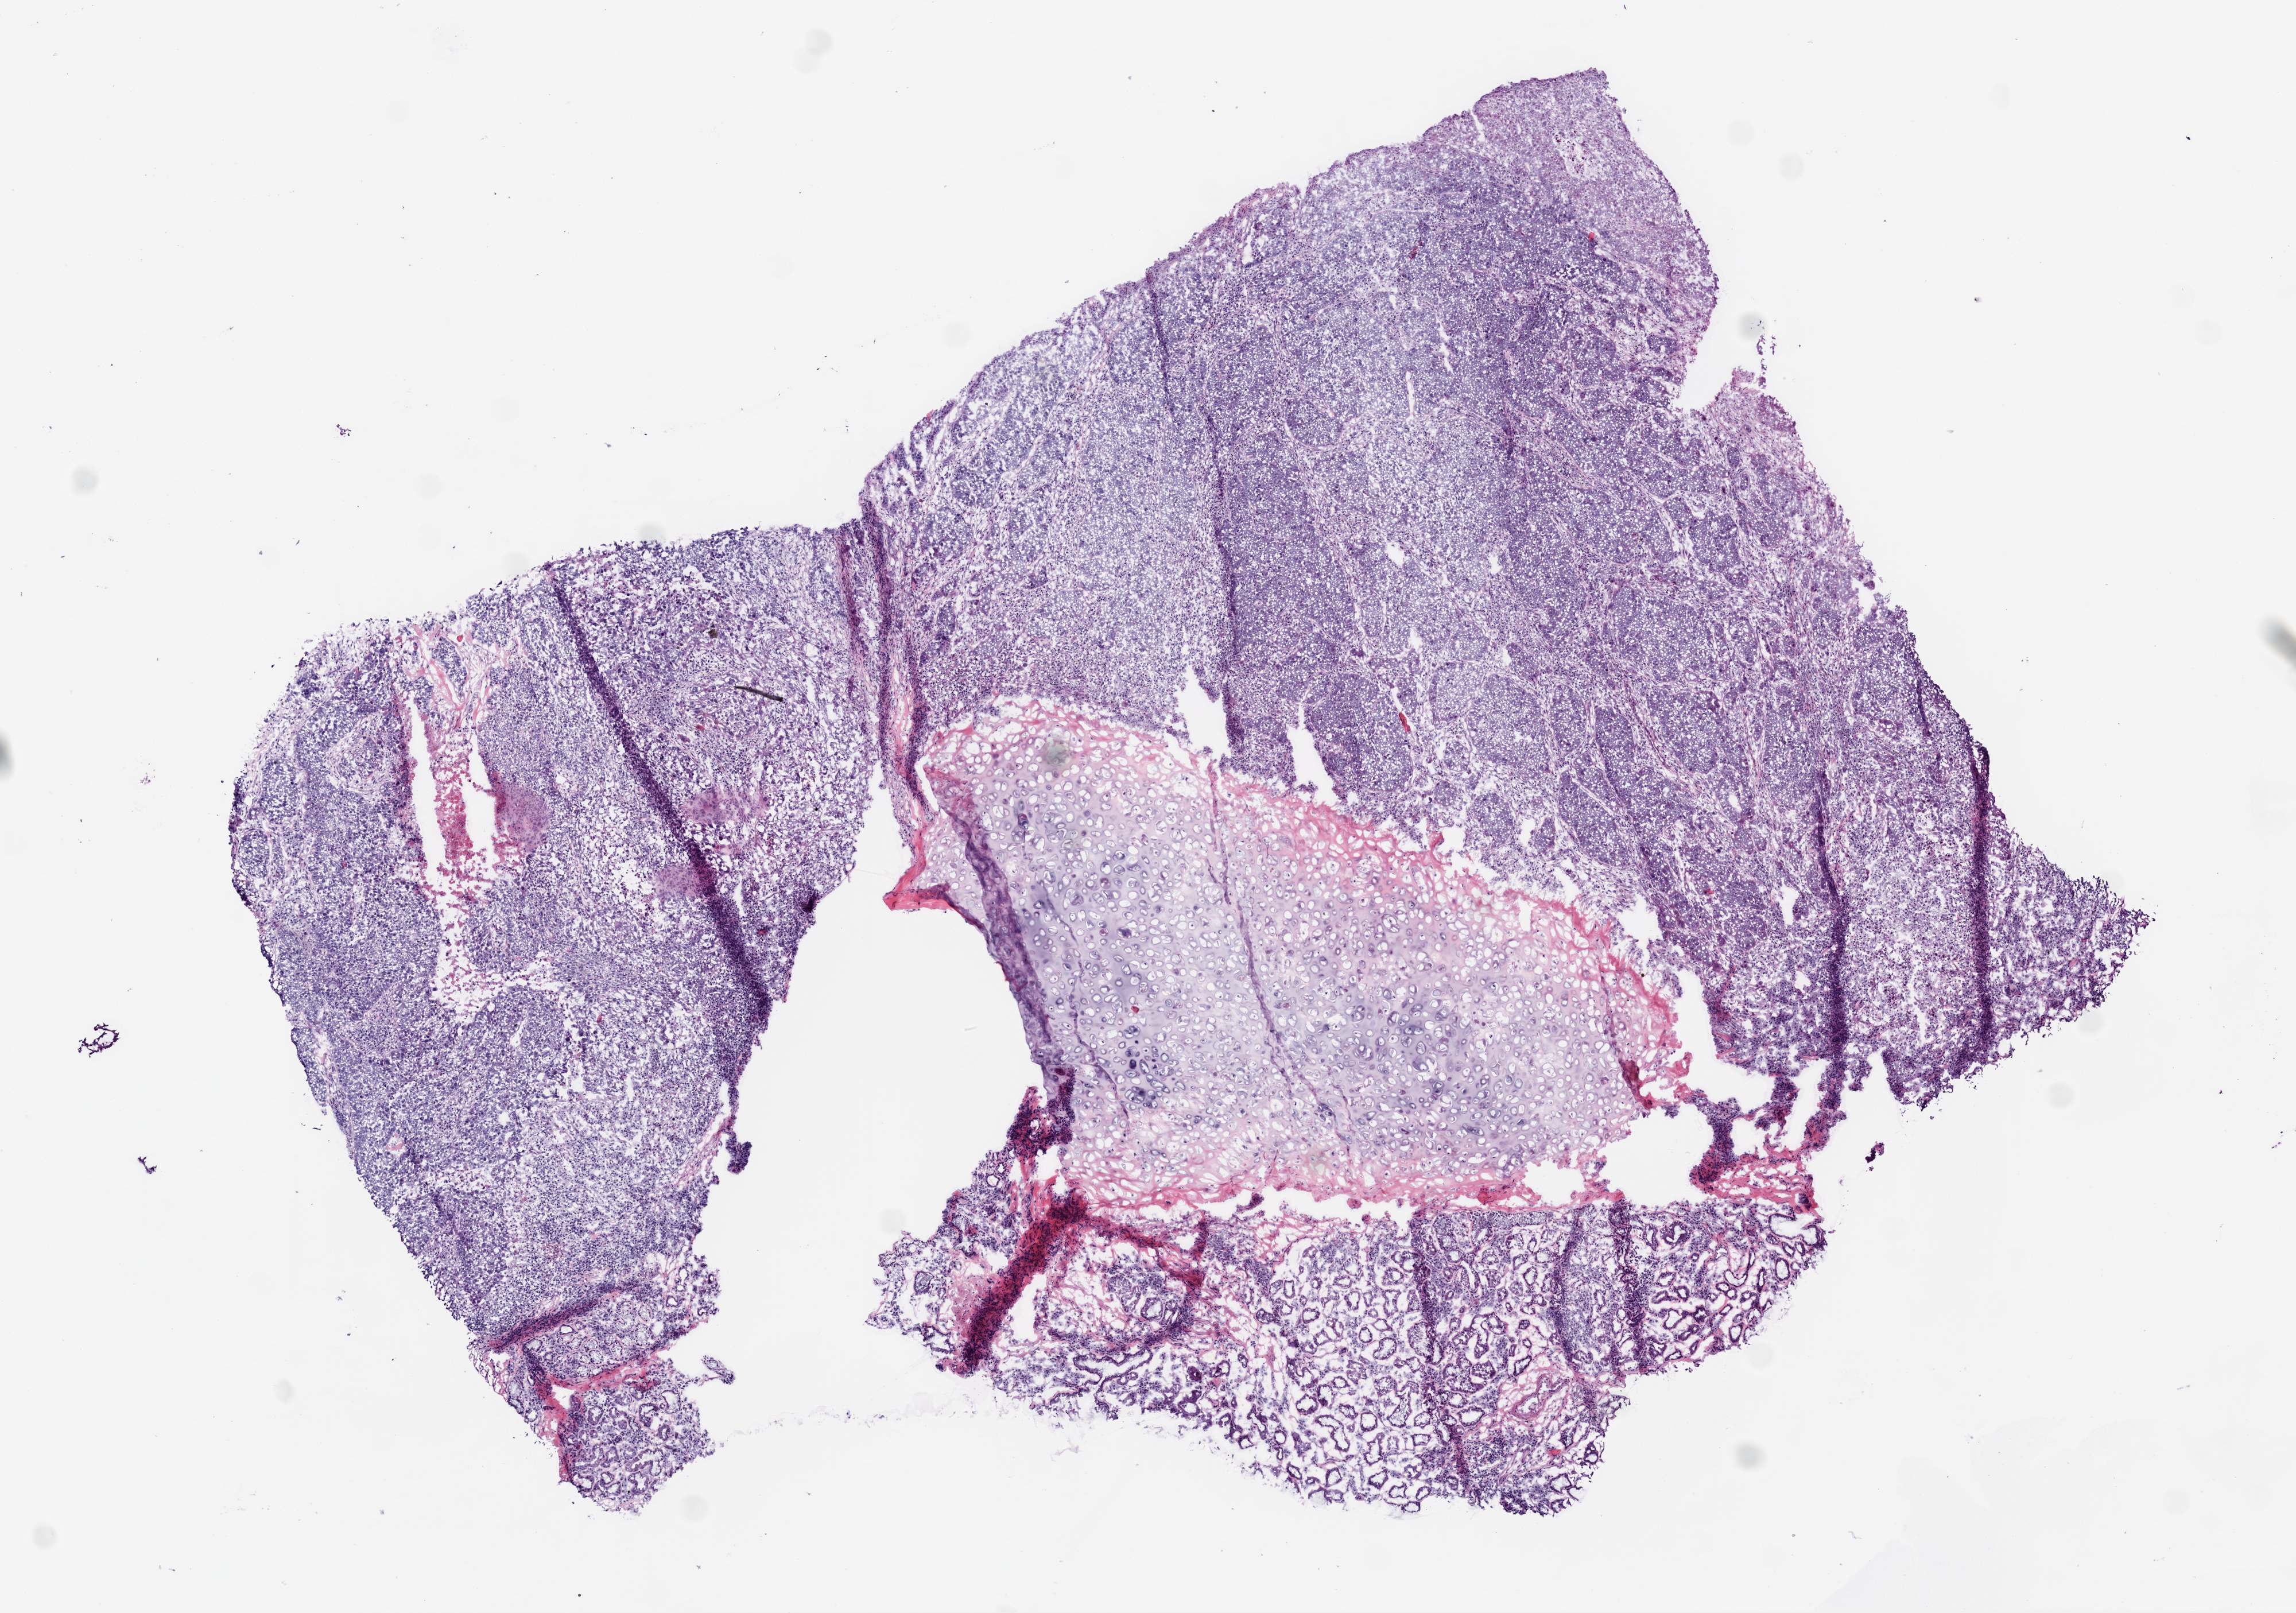
Digitized H&E tissue section (whole slide), a low-resolution overview of the entire scanned area, about 8.0 x 5.6 mm, frozen section, sample: primary tumour, lung. Female patient; age at initial diagnosis 63 years. Pathologist review of this section (percent, as recorded): tumour cells 55%, tumour nuclei 70%, normal cells 30%, stromal cells 10%, necrosis 5%. Inflammatory infiltration, as recorded: lymphocyte infiltration 15%.
• AJCC pathologic stage: IIIA
• histologic diagnosis: Squamous cell carcinoma, NOS (upper lobe, lung)